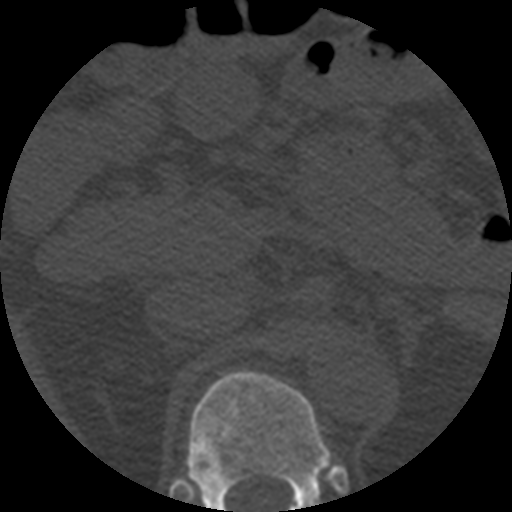
CT including the spine, one axial slice; slice 219 of 508 in the series (ordered by position); 120 kVp; bone window (W 1800 / L 400 HU); 1.25 mm slice thickness; 512 × 512 image matrix, field of view 160 × 160 mm. Patient age 57 years. From the clinical record (not read from this slice): primary cancer: prostate.
Outlined on this slice (semi-automatically segmented with operator editing):
- T12 vertebra: bounding box <186,370,332,512> (left, top, right, bottom; pixels)